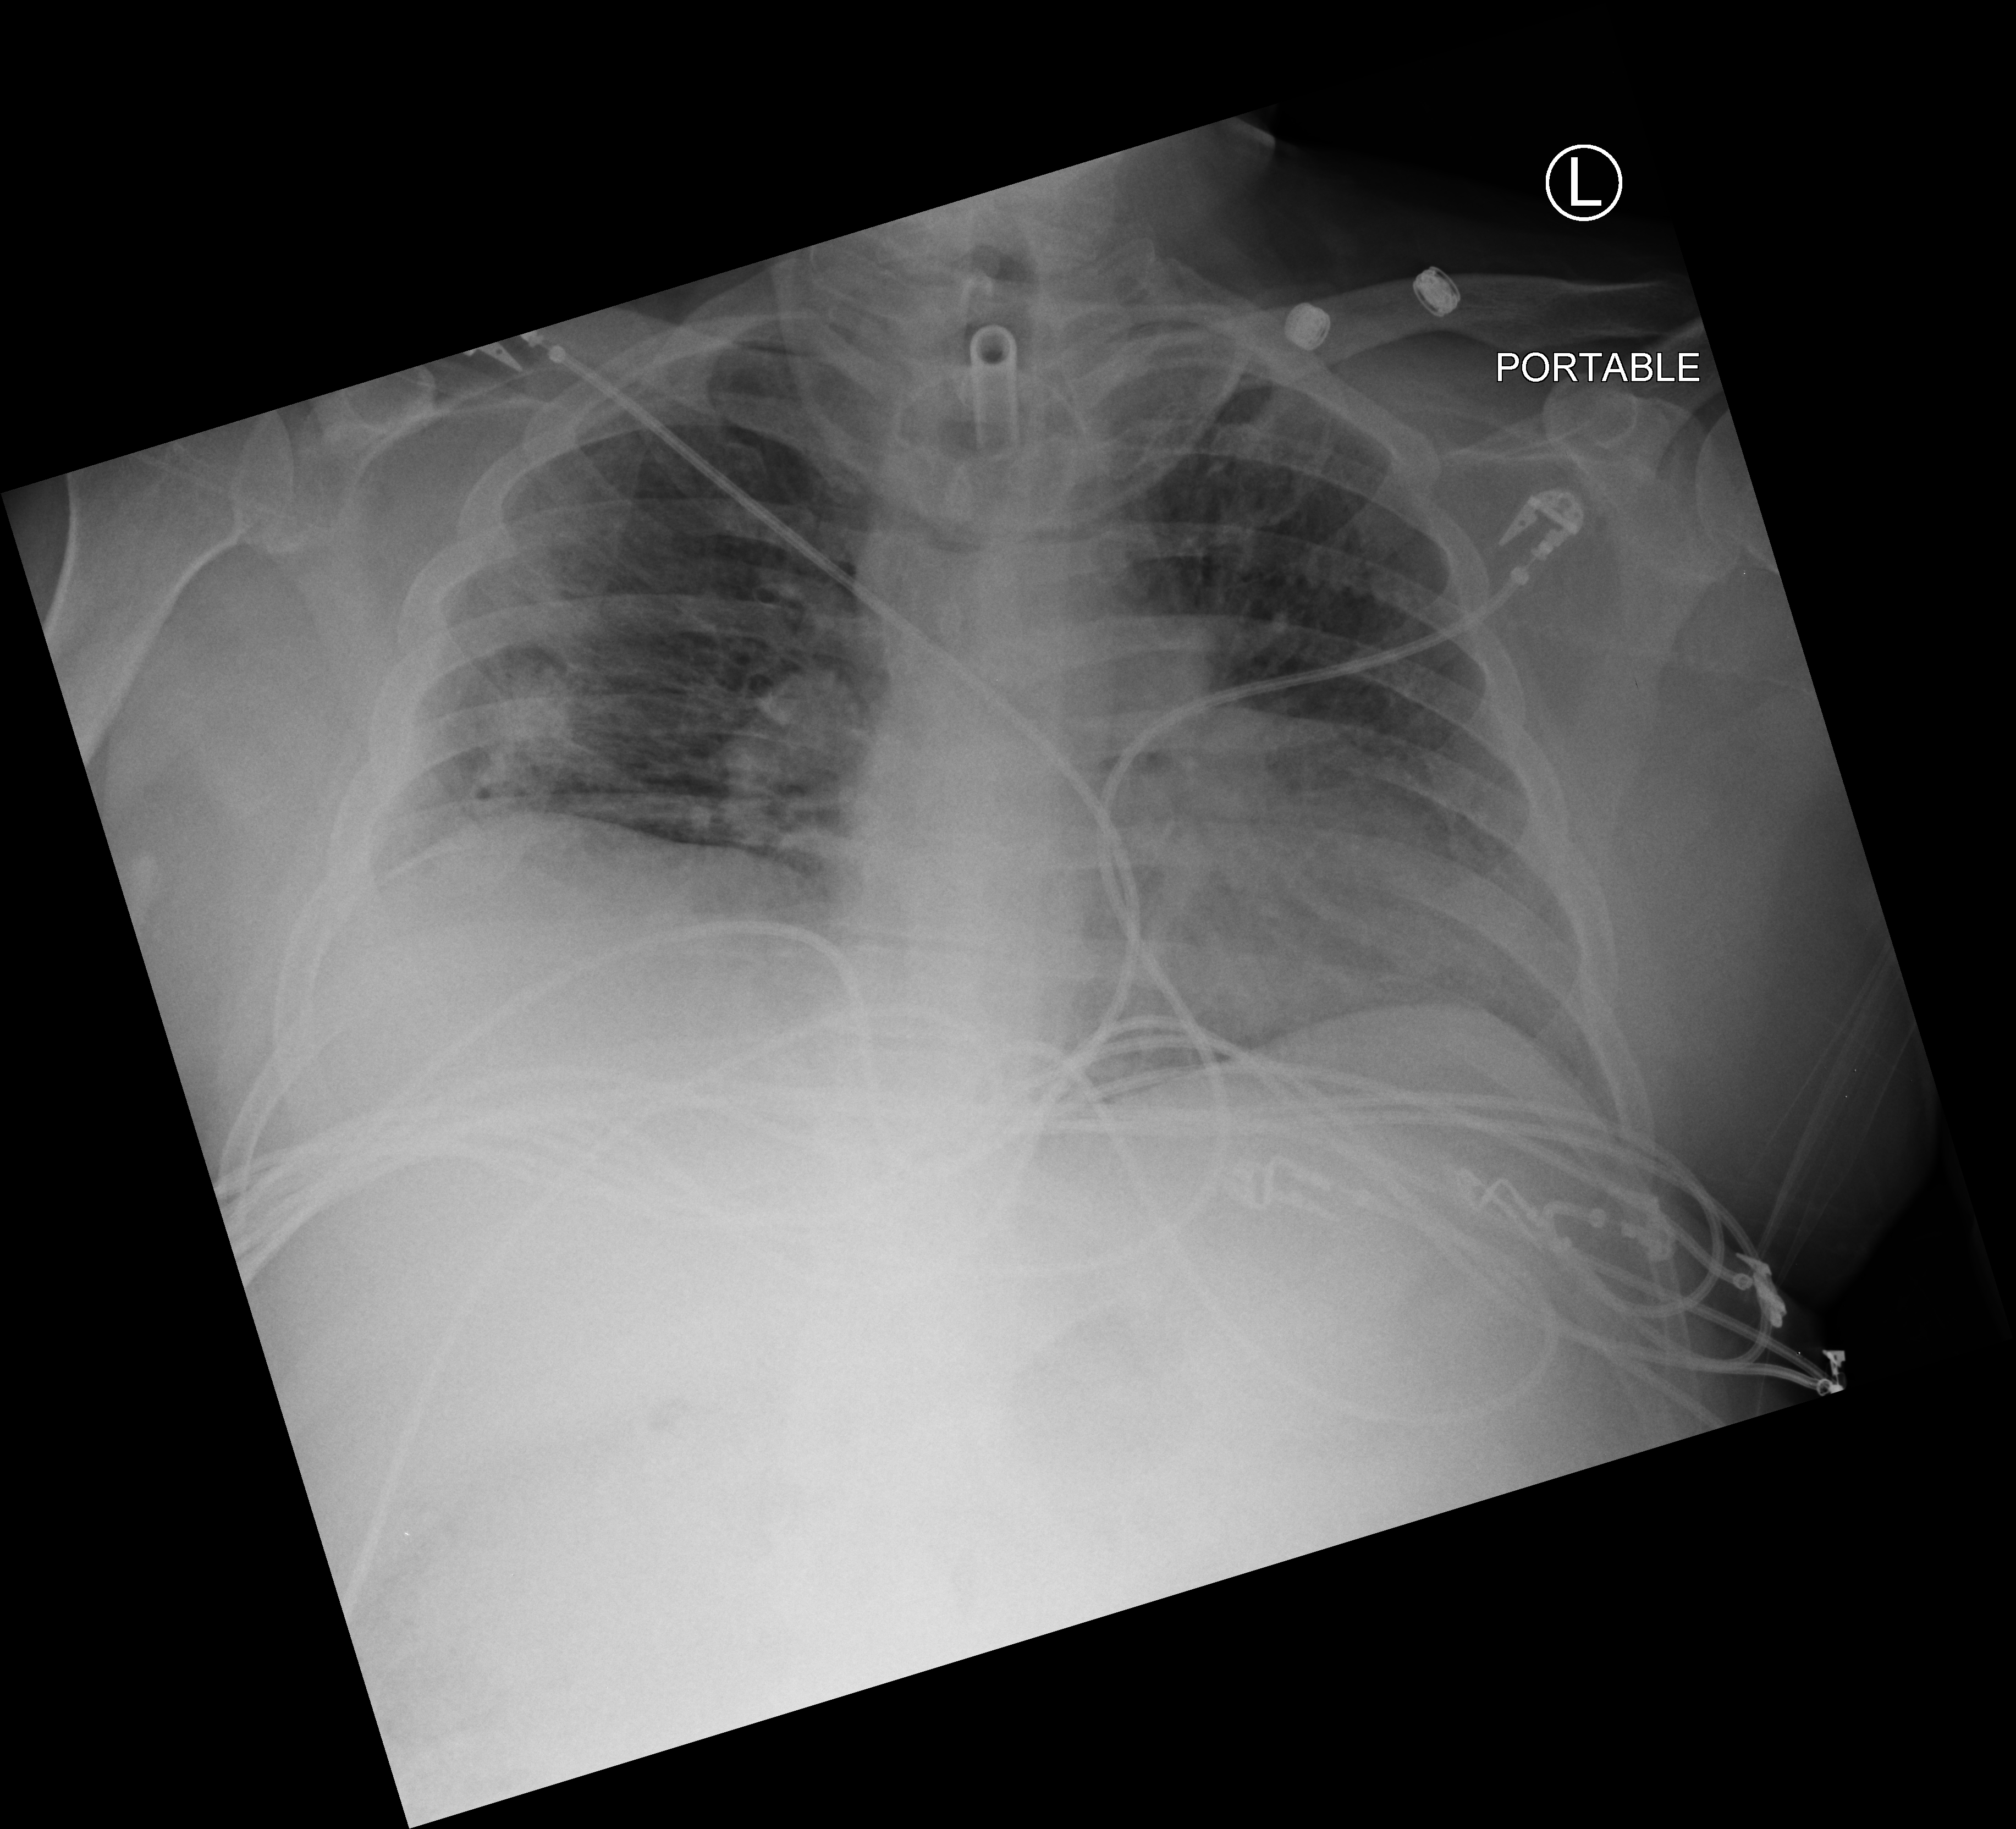
Portable chest radiograph; anteroposterior (AP) projection. Patient hospitalised with COVID-19; male, aged 18–59 years.
From the hospital-stay record, not from the radiograph (when in the stay this image was taken is not recorded): mechanically ventilated during this hospital stay: yes; hypertension (admission record): yes; admitted to intensive care during this hospital stay: yes.